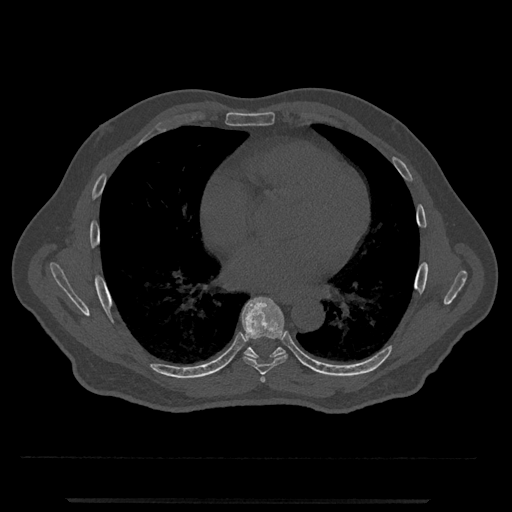
CT including the spine, one axial slice; position 663 of 797 along the scan axis; reconstruction kernel Br40s/3; bone window (W 1800 / L 400 HU); 0.5 mm slice thickness; 512 × 512 image matrix, field of view 419 × 419 mm. Male patient, age 63 years. From the clinical record (not read from this slice): primary cancer: prostate.
Annotated regions visible in this slice (semi-automatic segmentation, software-assisted and operator-edited):
- T6 vertebra: box from (x=260, y=375) to (x=266, y=383) px
- T7 vertebra: (x=242, y=296)–(x=288, y=375)
- T8 vertebra: (x=244, y=338)–(x=286, y=359)